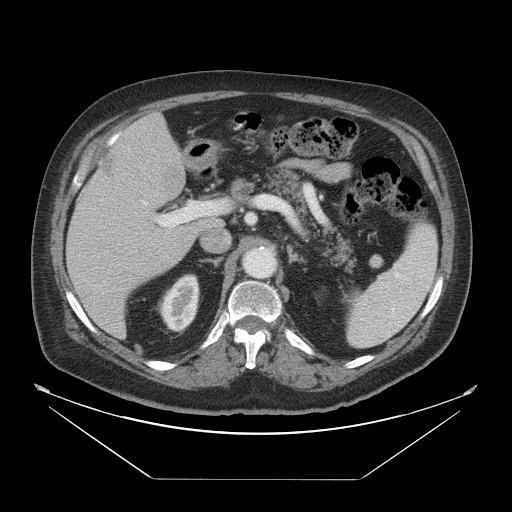
Contrast-enhanced abdominal CT, one axial slice; slice 29 of 45 in the series (ordered by position); reconstruction kernel STANDARD; 120 kVp; intravenous contrast given; soft-tissue window (W 400 / L 40 HU); 5 mm slice thickness; 512 × 512 image matrix, field of view 463 × 463 mm. Male patient, age 87 years. From the clinical record (not read from this slice): diagnosis: colorectal cancer liver metastases, imaged before liver resection; multiple liver metastases: no; largest metastasis: 4.5 cm; disease in both lobes: yes.
Annotated regions visible in this slice (manually delineated by an expert):
- liver: bounding box (x1, y1, x2, y2) in pixels: (66, 114, 223, 339)
- planned liver remnant (the part of the liver to remain after resection): (122, 114, 182, 159)
- portal vein (with intrahepatic branches): (141, 201, 209, 233)
- liver metastasis: (161, 164, 186, 194)
- liver metastasis: (99, 153, 122, 185)